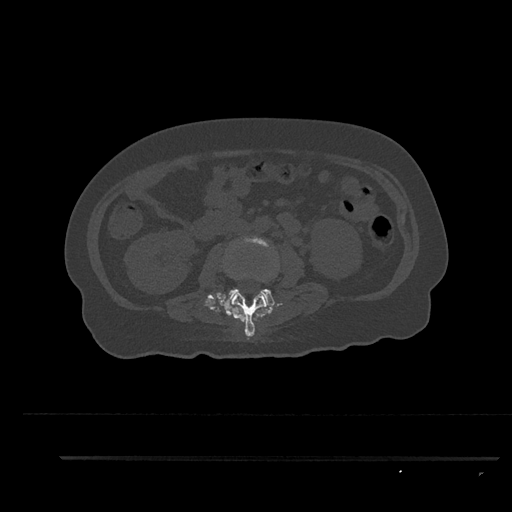
CT including the spine, one axial slice; reconstruction kernel Br40s/3; 120 kVp; bone window (W 1800 / L 400 HU); 0.5 mm slice thickness; 512 × 512 image matrix, field of view 408 × 408 mm. Female patient, age 44 years. Case-level facts recorded for this patient, not image findings: primary cancer: renal; vertebrae with lytic lesions (as recorded): L1.
Outlined on this slice (semi-automatically segmented with operator editing):
- L2 vertebra: box from (x=226, y=292) to (x=268, y=337) px
- L3 vertebra: (x=223, y=236)–(x=276, y=307)